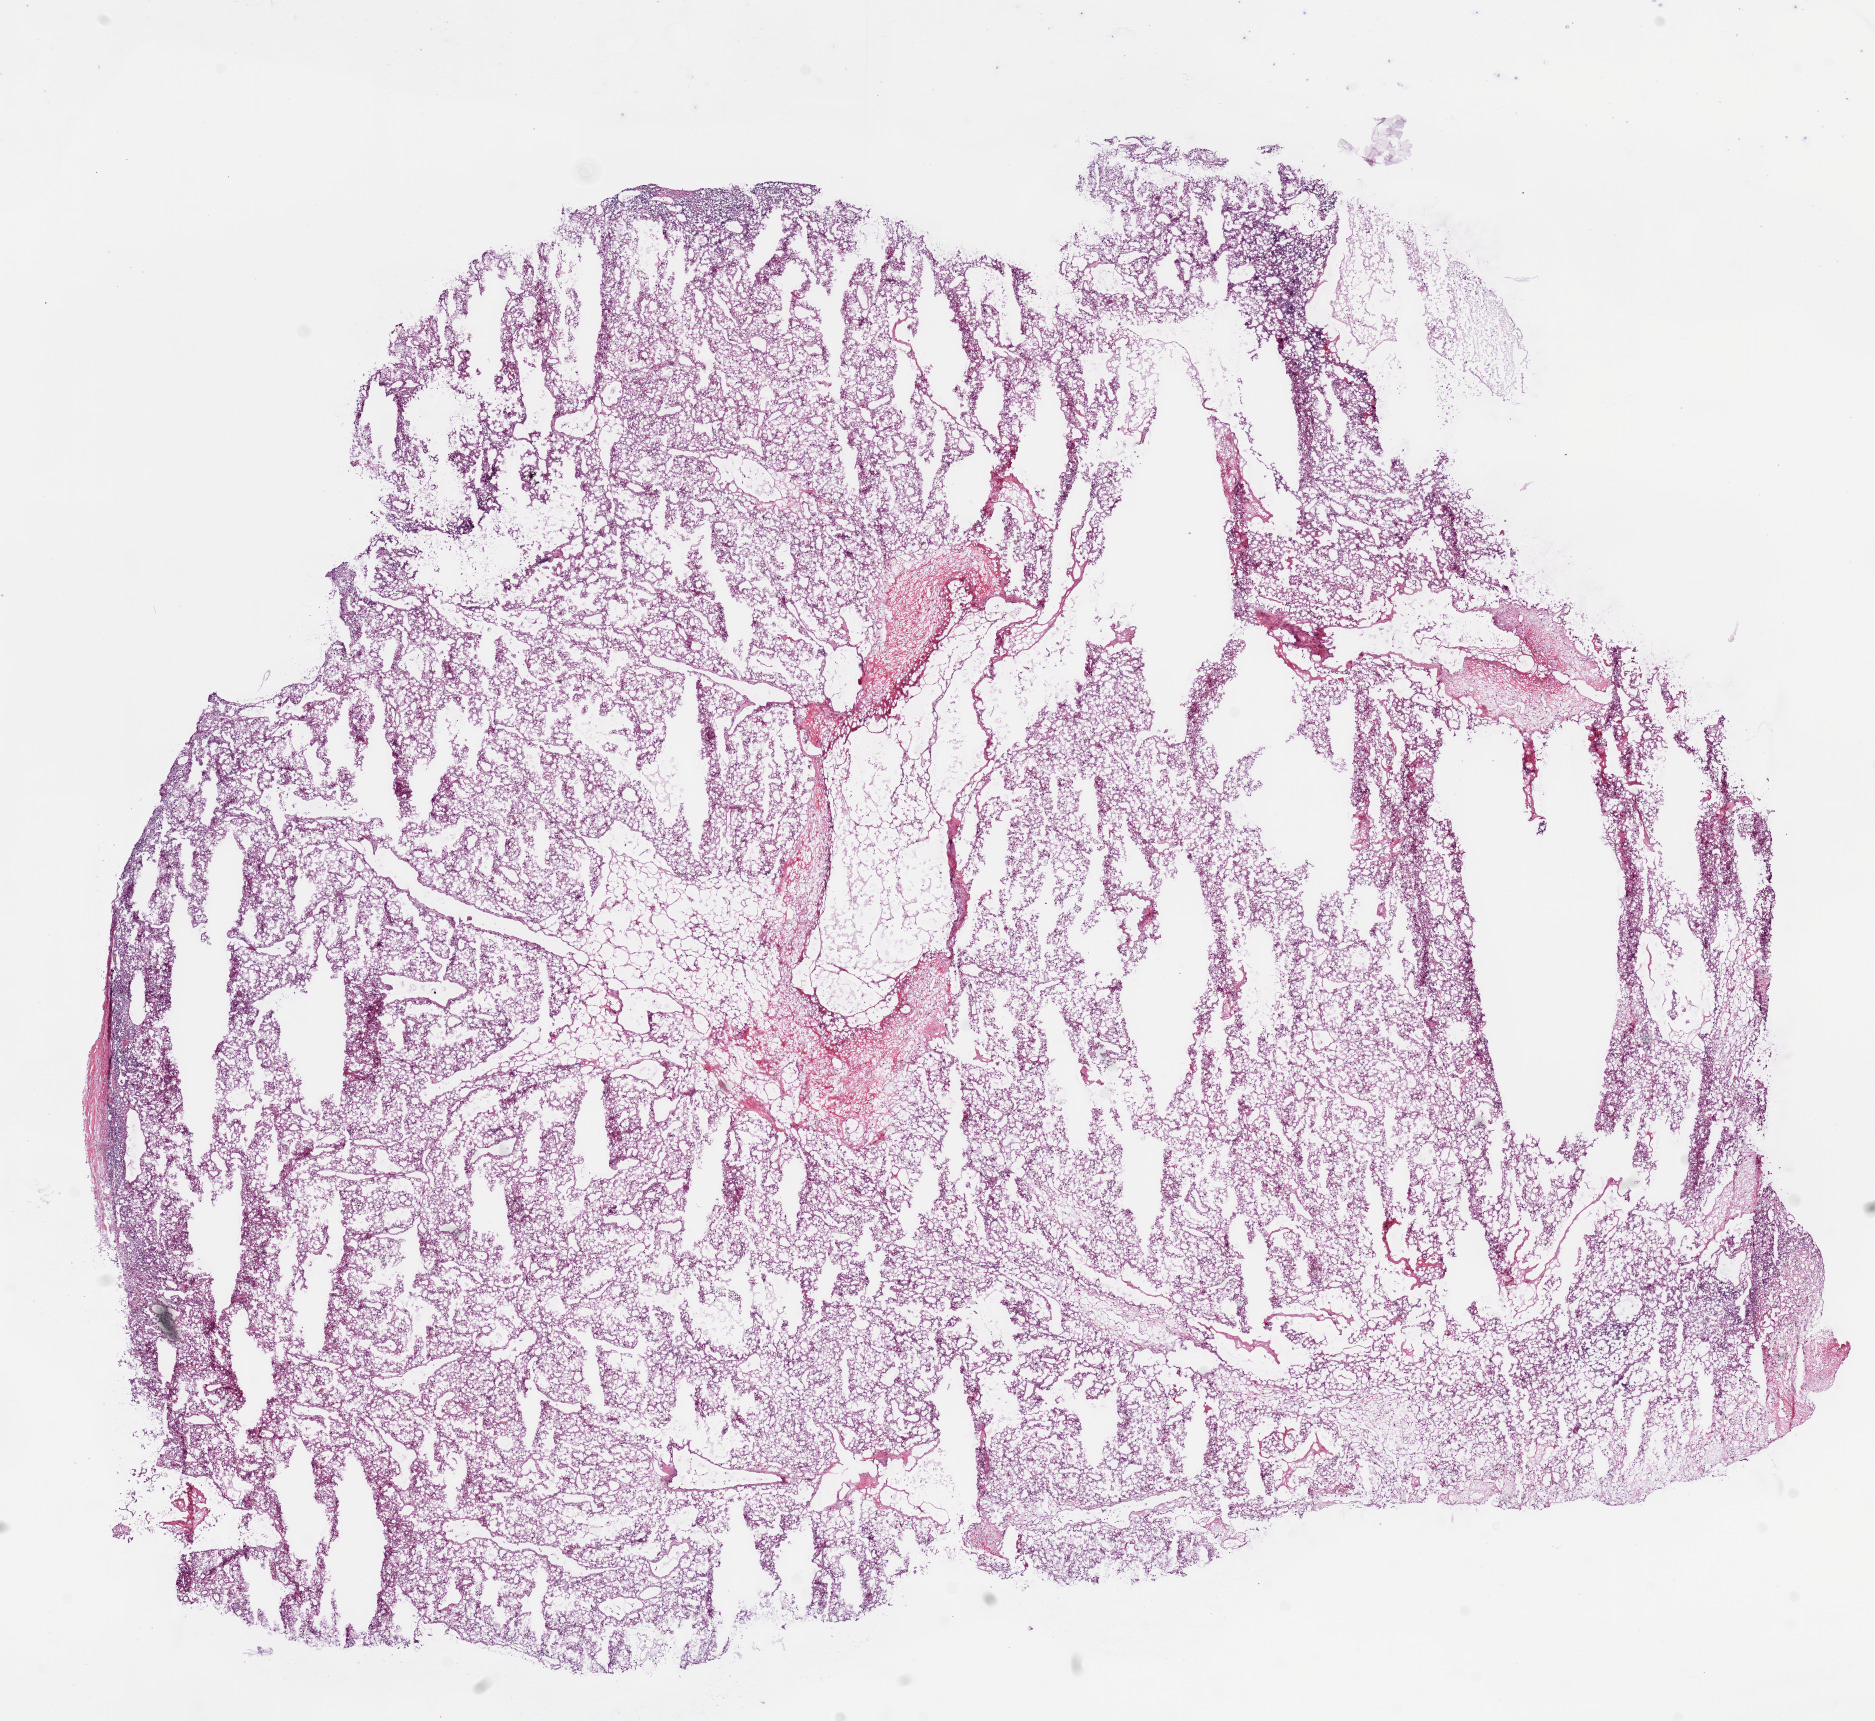
Digitized Hematoxylin and eosin (H&E) stained tissue section (whole slide), a low-resolution overview of the entire scanned area, about 15.0 x 13.8 mm. Frozen section from the bottom of the tissue portion. Kidney, primary tumour sample. Male, age 46 years at initial diagnosis.
Diagnosis: Clear cell adenocarcinoma, NOS.